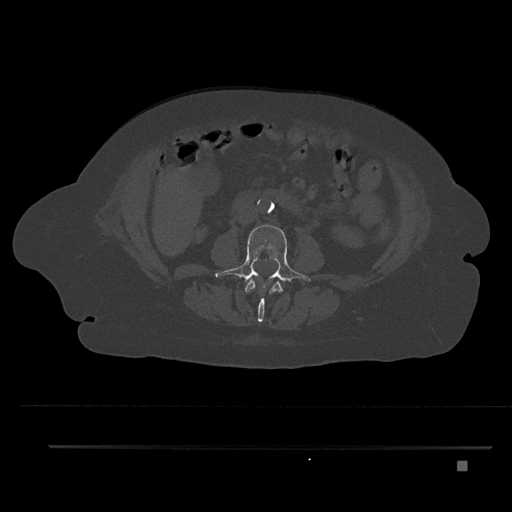
CT including the spine, one axial slice. Position 136 of 797 along the scan axis. Reconstruction kernel Br40s/3. Bone window (W 1800 / L 400 HU). 0.5 mm slice thickness. 512 × 512 image matrix, field of view 437 × 437 mm. Patient: female, 76 years. Case-level facts recorded for this patient, not image findings: primary cancer: lung.
Annotated regions visible in this slice (semi-automatically segmented with operator editing):
- L2 vertebra: box from (x=245, y=279) to (x=283, y=322) px
- L3 vertebra: (x=215, y=224)–(x=311, y=289)